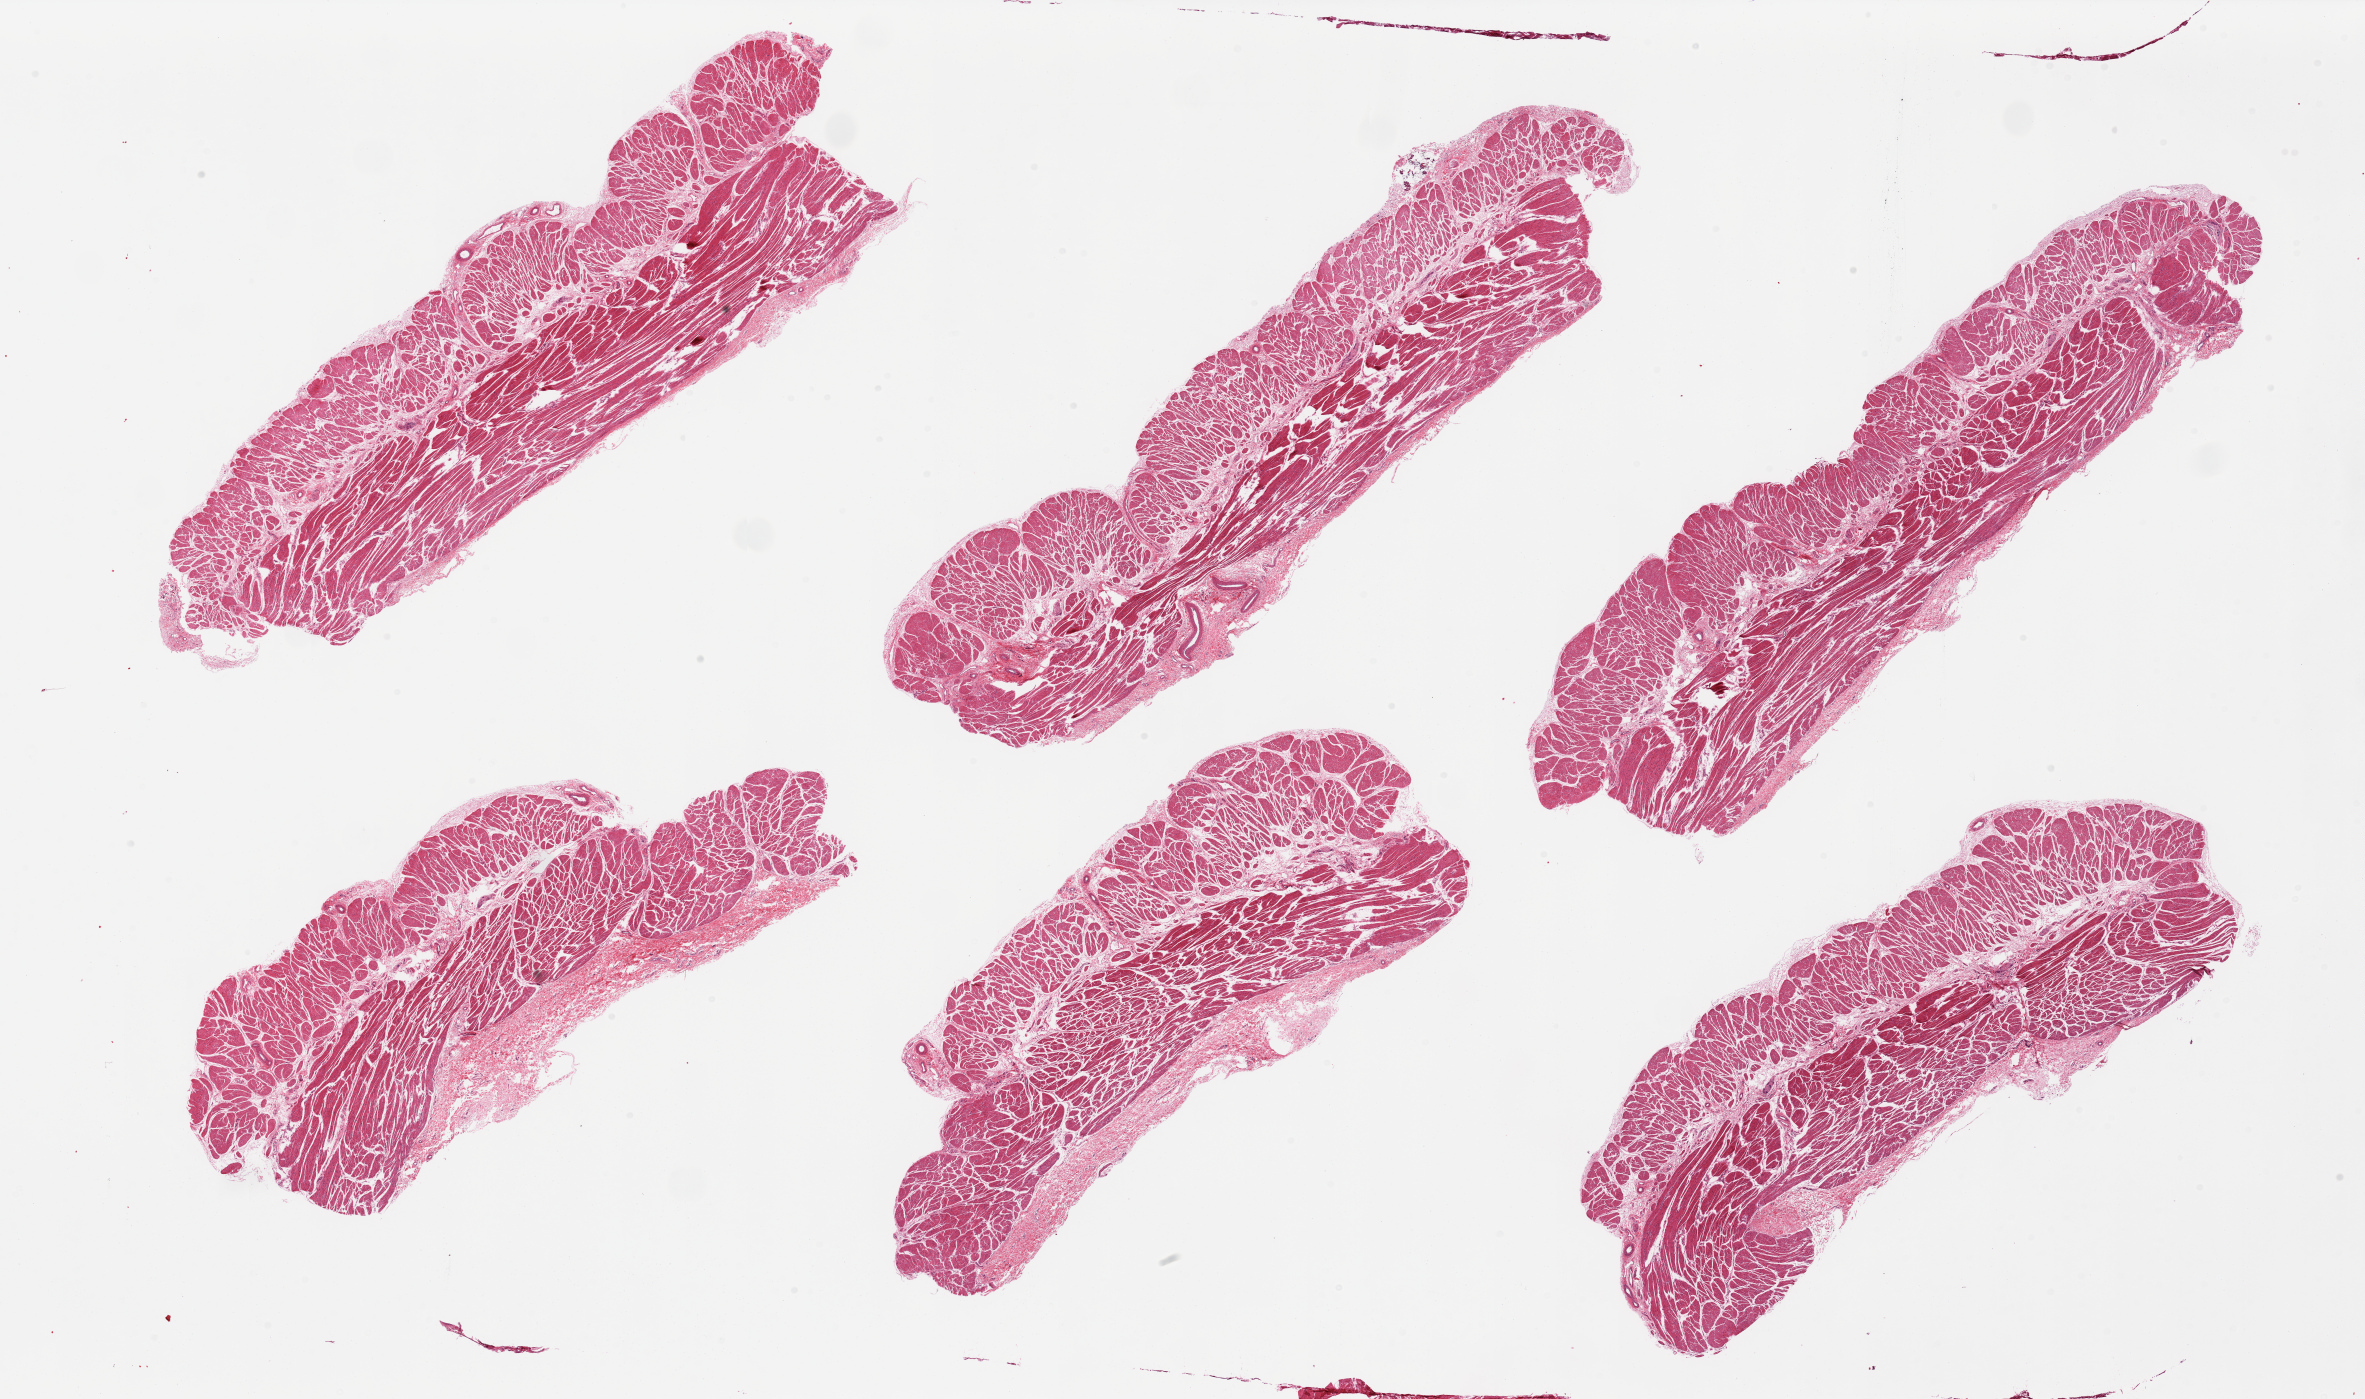
Hematoxylin and eosin (H&E) whole-slide image, whole scanned area (about 37.4 x 22.1 mm, slide scanned at 20x) shown as a low-resolution overview, PAXgene-fixed paraffin-embedded (PFPE) section, section of esophageal muscle (target tissue), donor tissue sample.
* reviewer comment on this tissue sample: 6 pieces, well trimmed